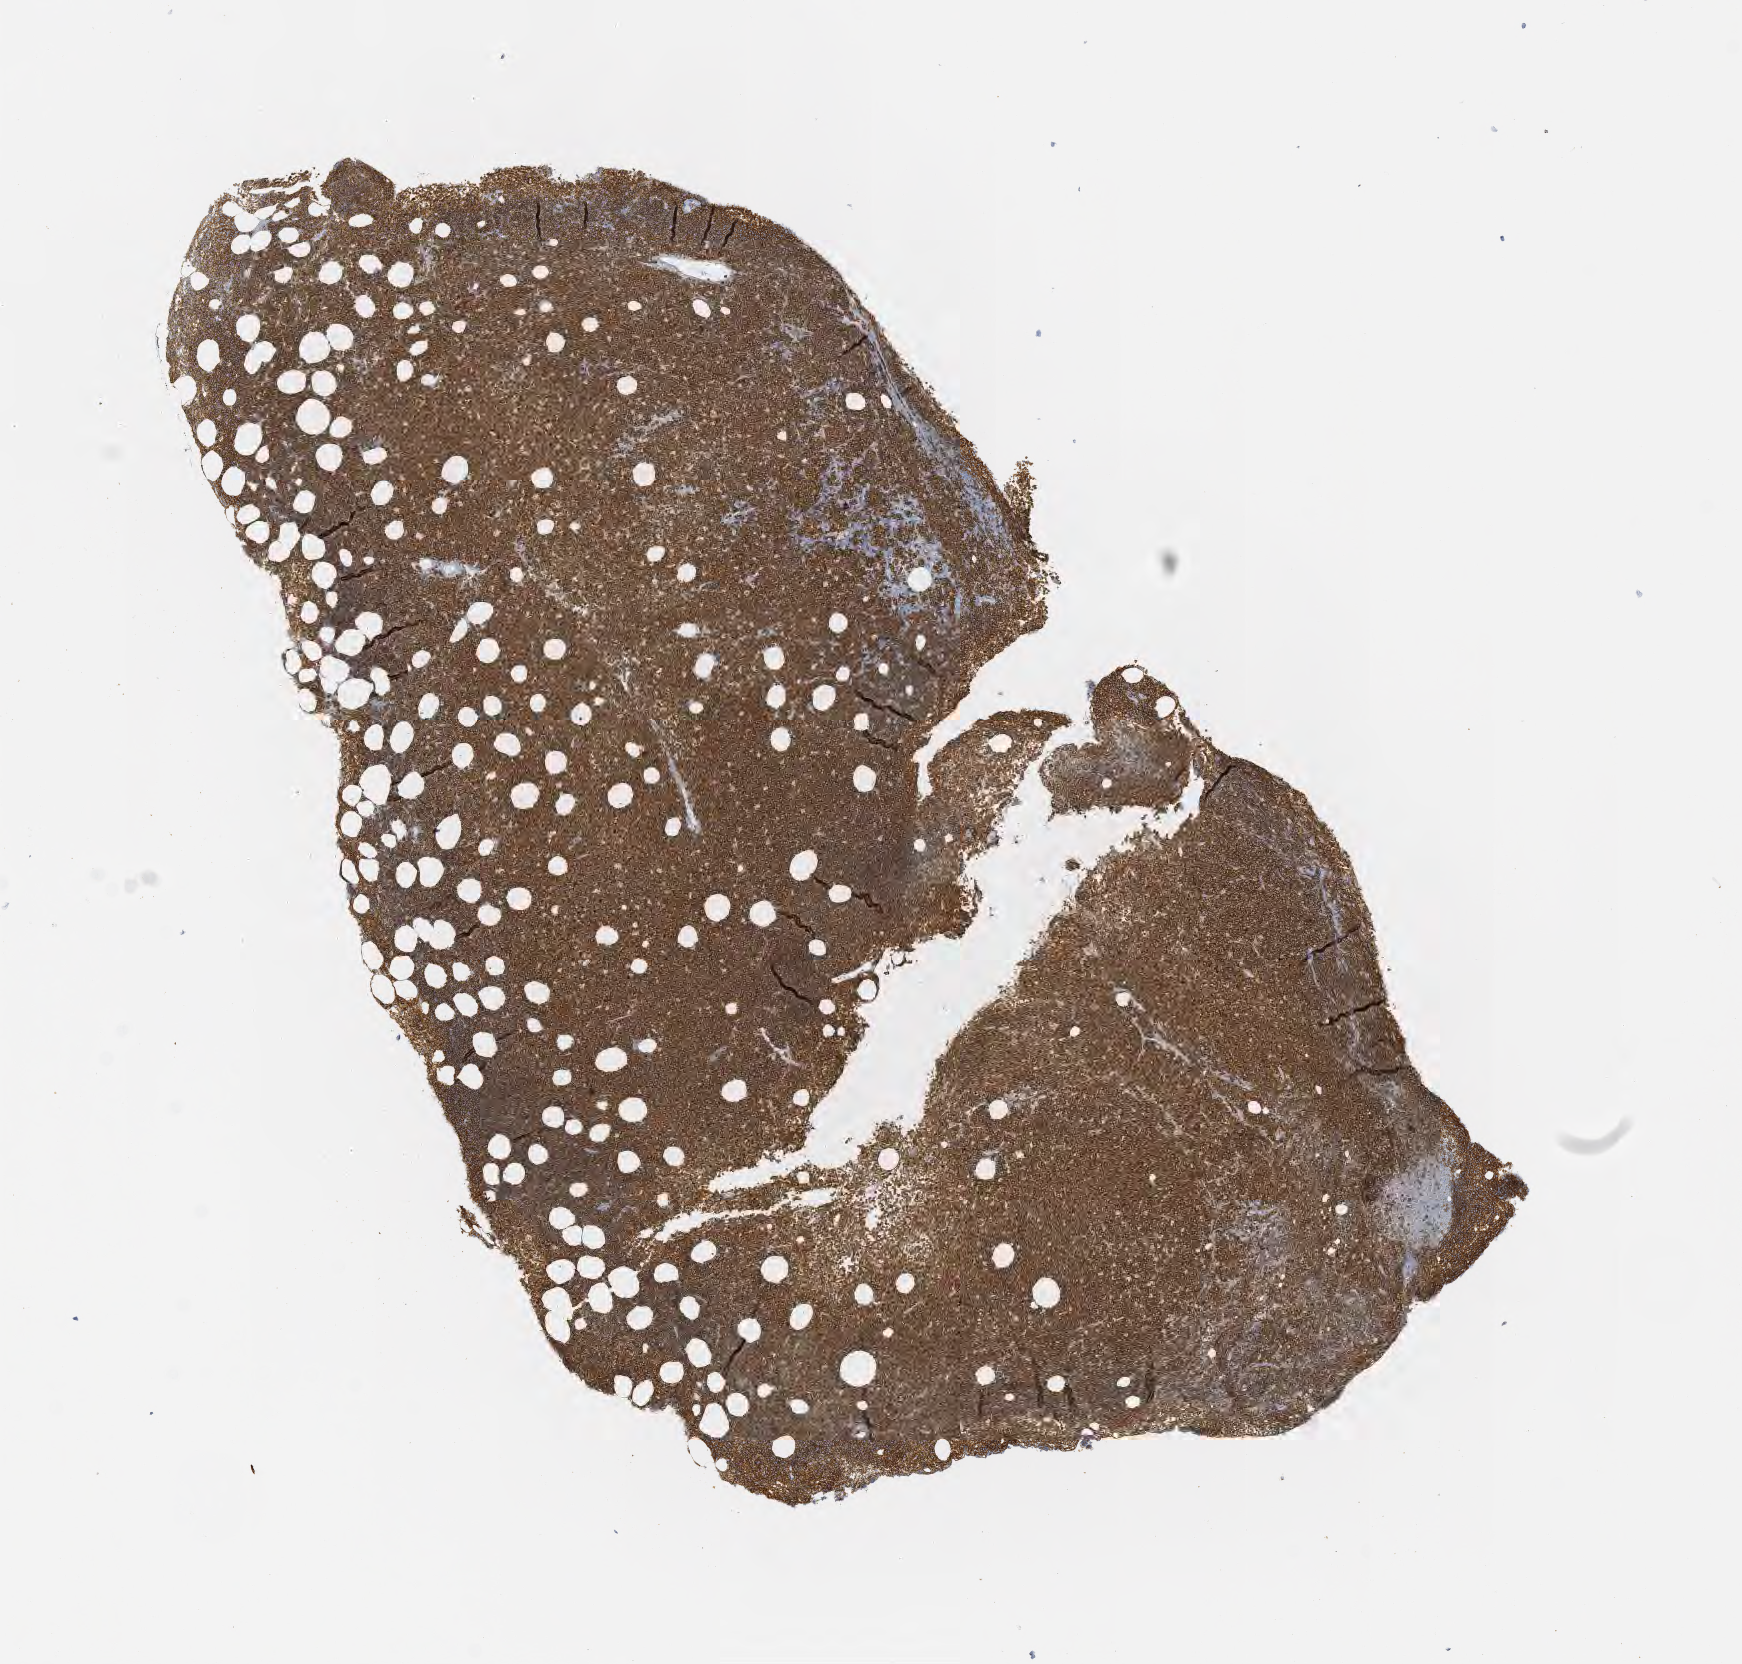
Immunohistochemistry (IHC) whole-slide image stained for CD20, shown as a low-resolution overview of the whole scanned area (about 7.0 x 6.7 mm), specimen: tumor tissue, anatomic site: bone marrow. Patient male; aged 70.
Diagnosis: Neoplasm, uncertain whether benign or malignant.